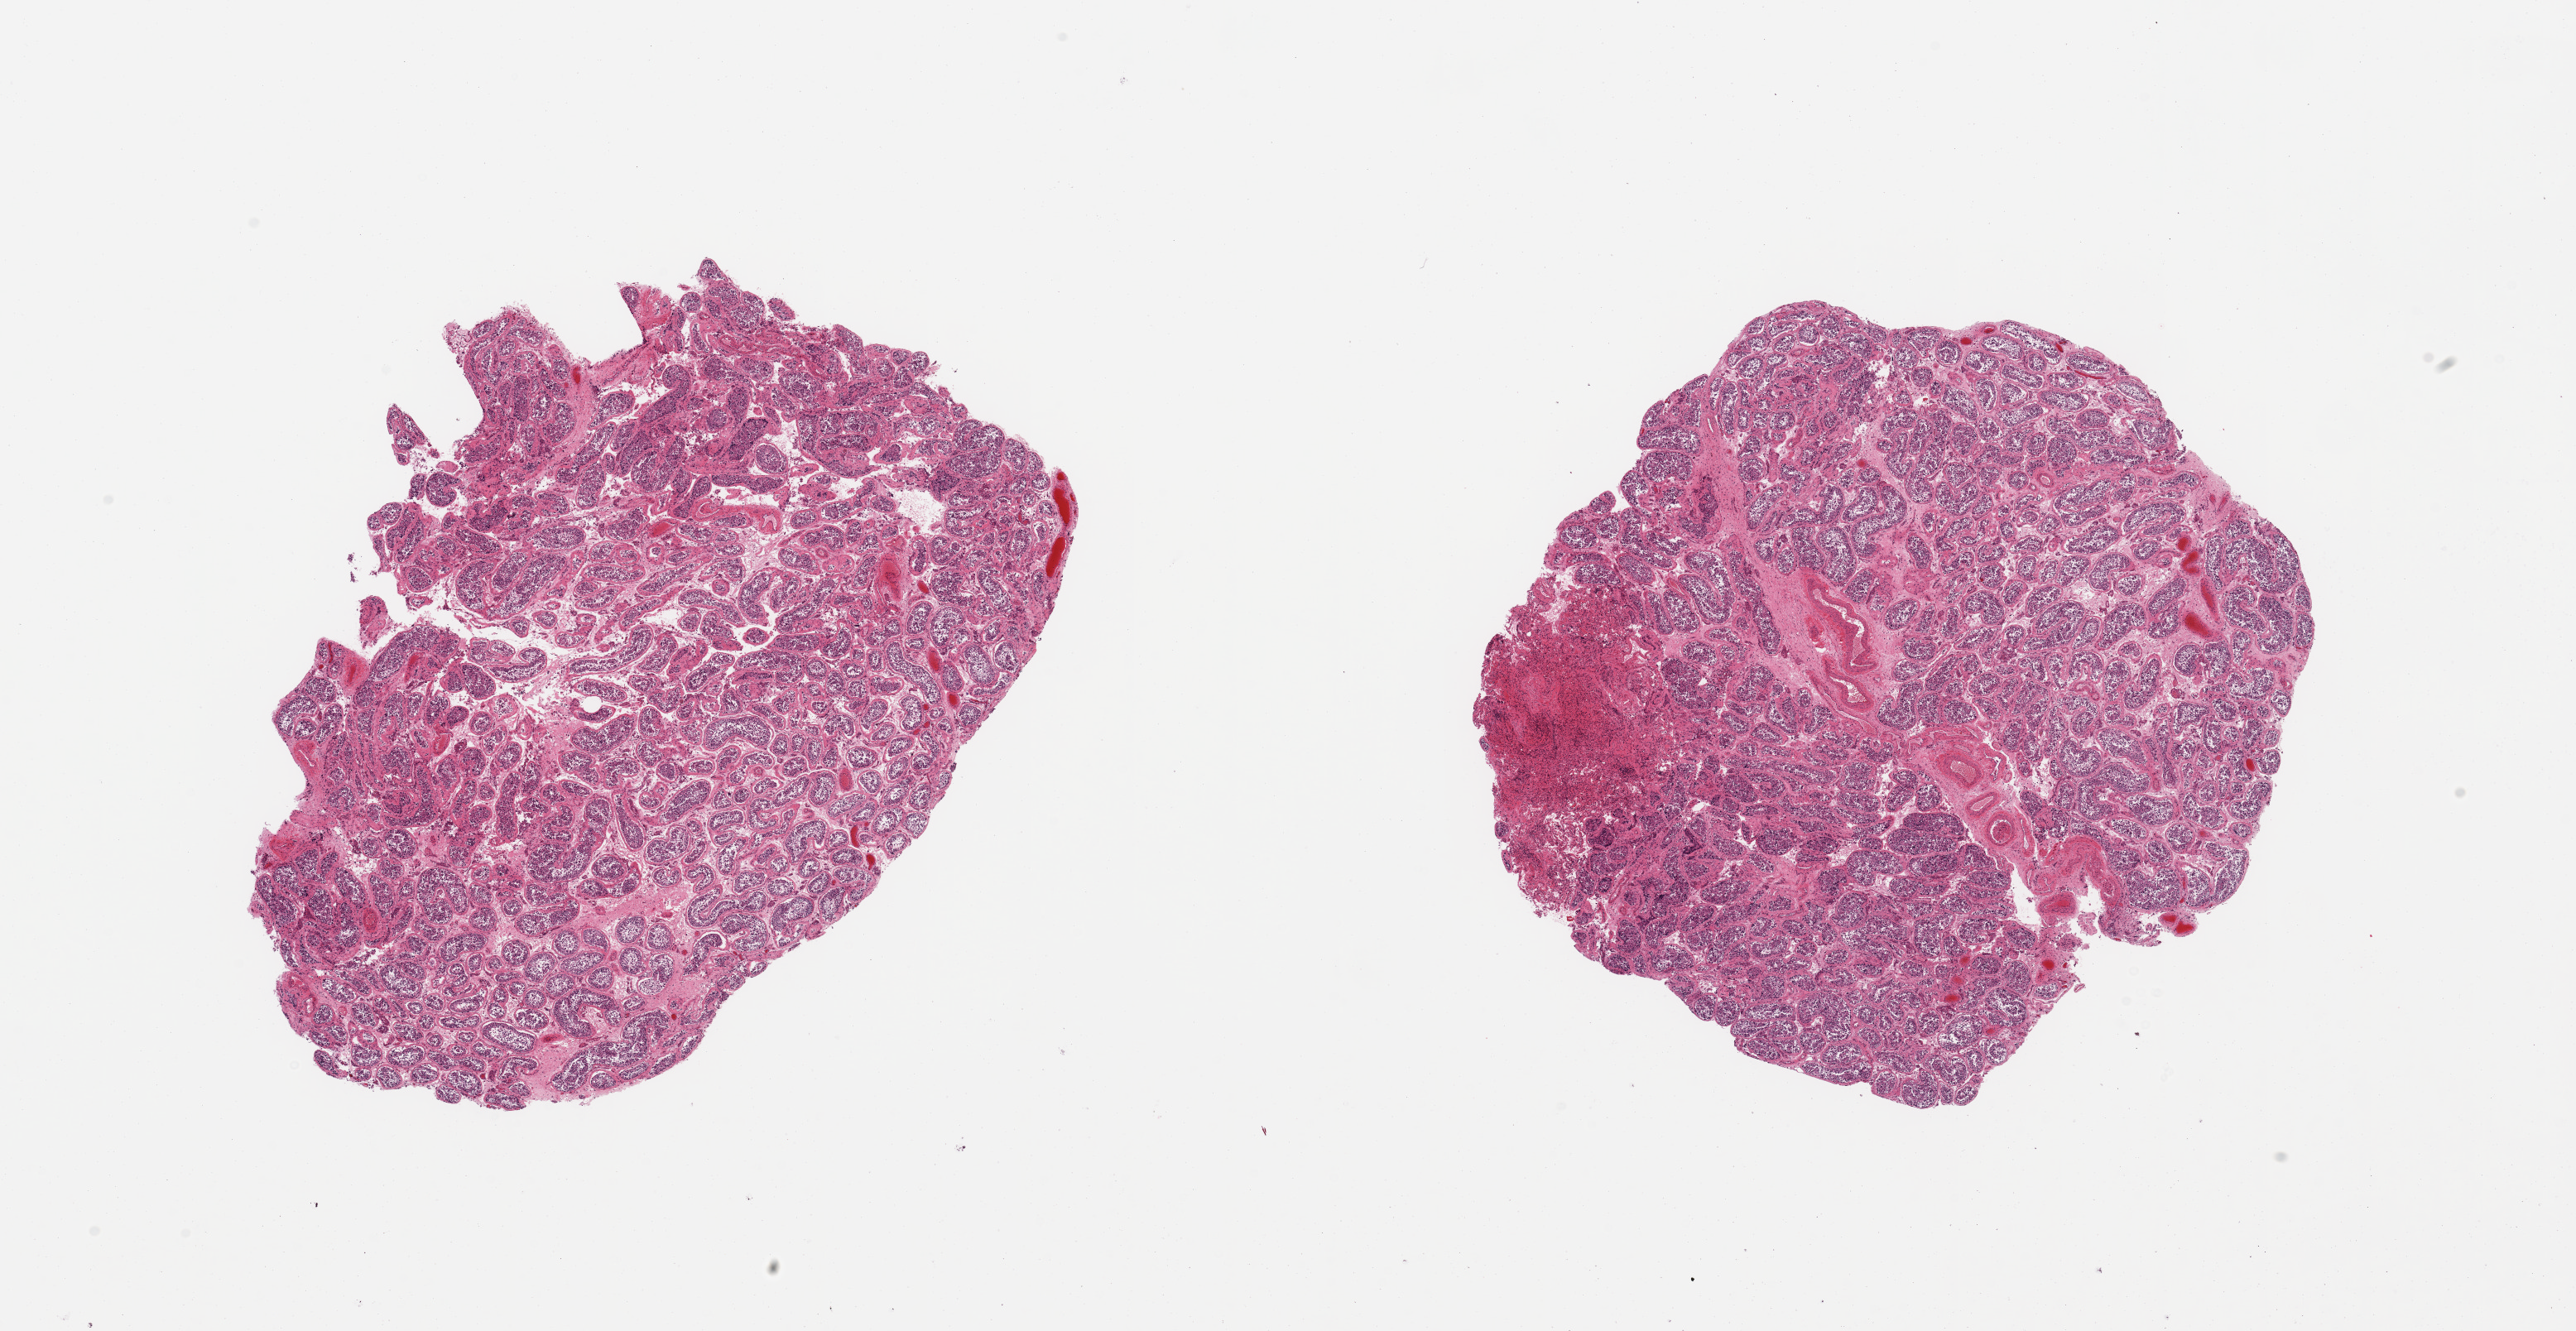
Whole-slide image, hematoxylin and eosin (H&E) stain, brightfield, shown as a low-resolution overview of the whole scanned area (about 24.6 x 12.7 mm, acquisition: 20x scan). PAXgene-fixed, paraffin-embedded tissue. Section of testis (target tissue). Donor tissue sample. Donor: male.
Reviewer comment on this tissue sample: 2 pieces; reduced numbers of mature sperm.